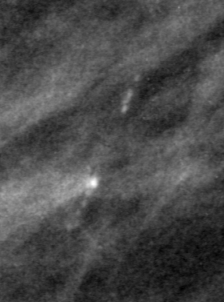
Cropped region of a digitized screen-film mammogram centred on a radiologist-marked abnormality; left breast; MLO view.
- Finding: calcifications, morphology fine linear branching, distribution linear; BI-RADS assessment category 4; pathology result (as recorded, not read from the image): malignant.